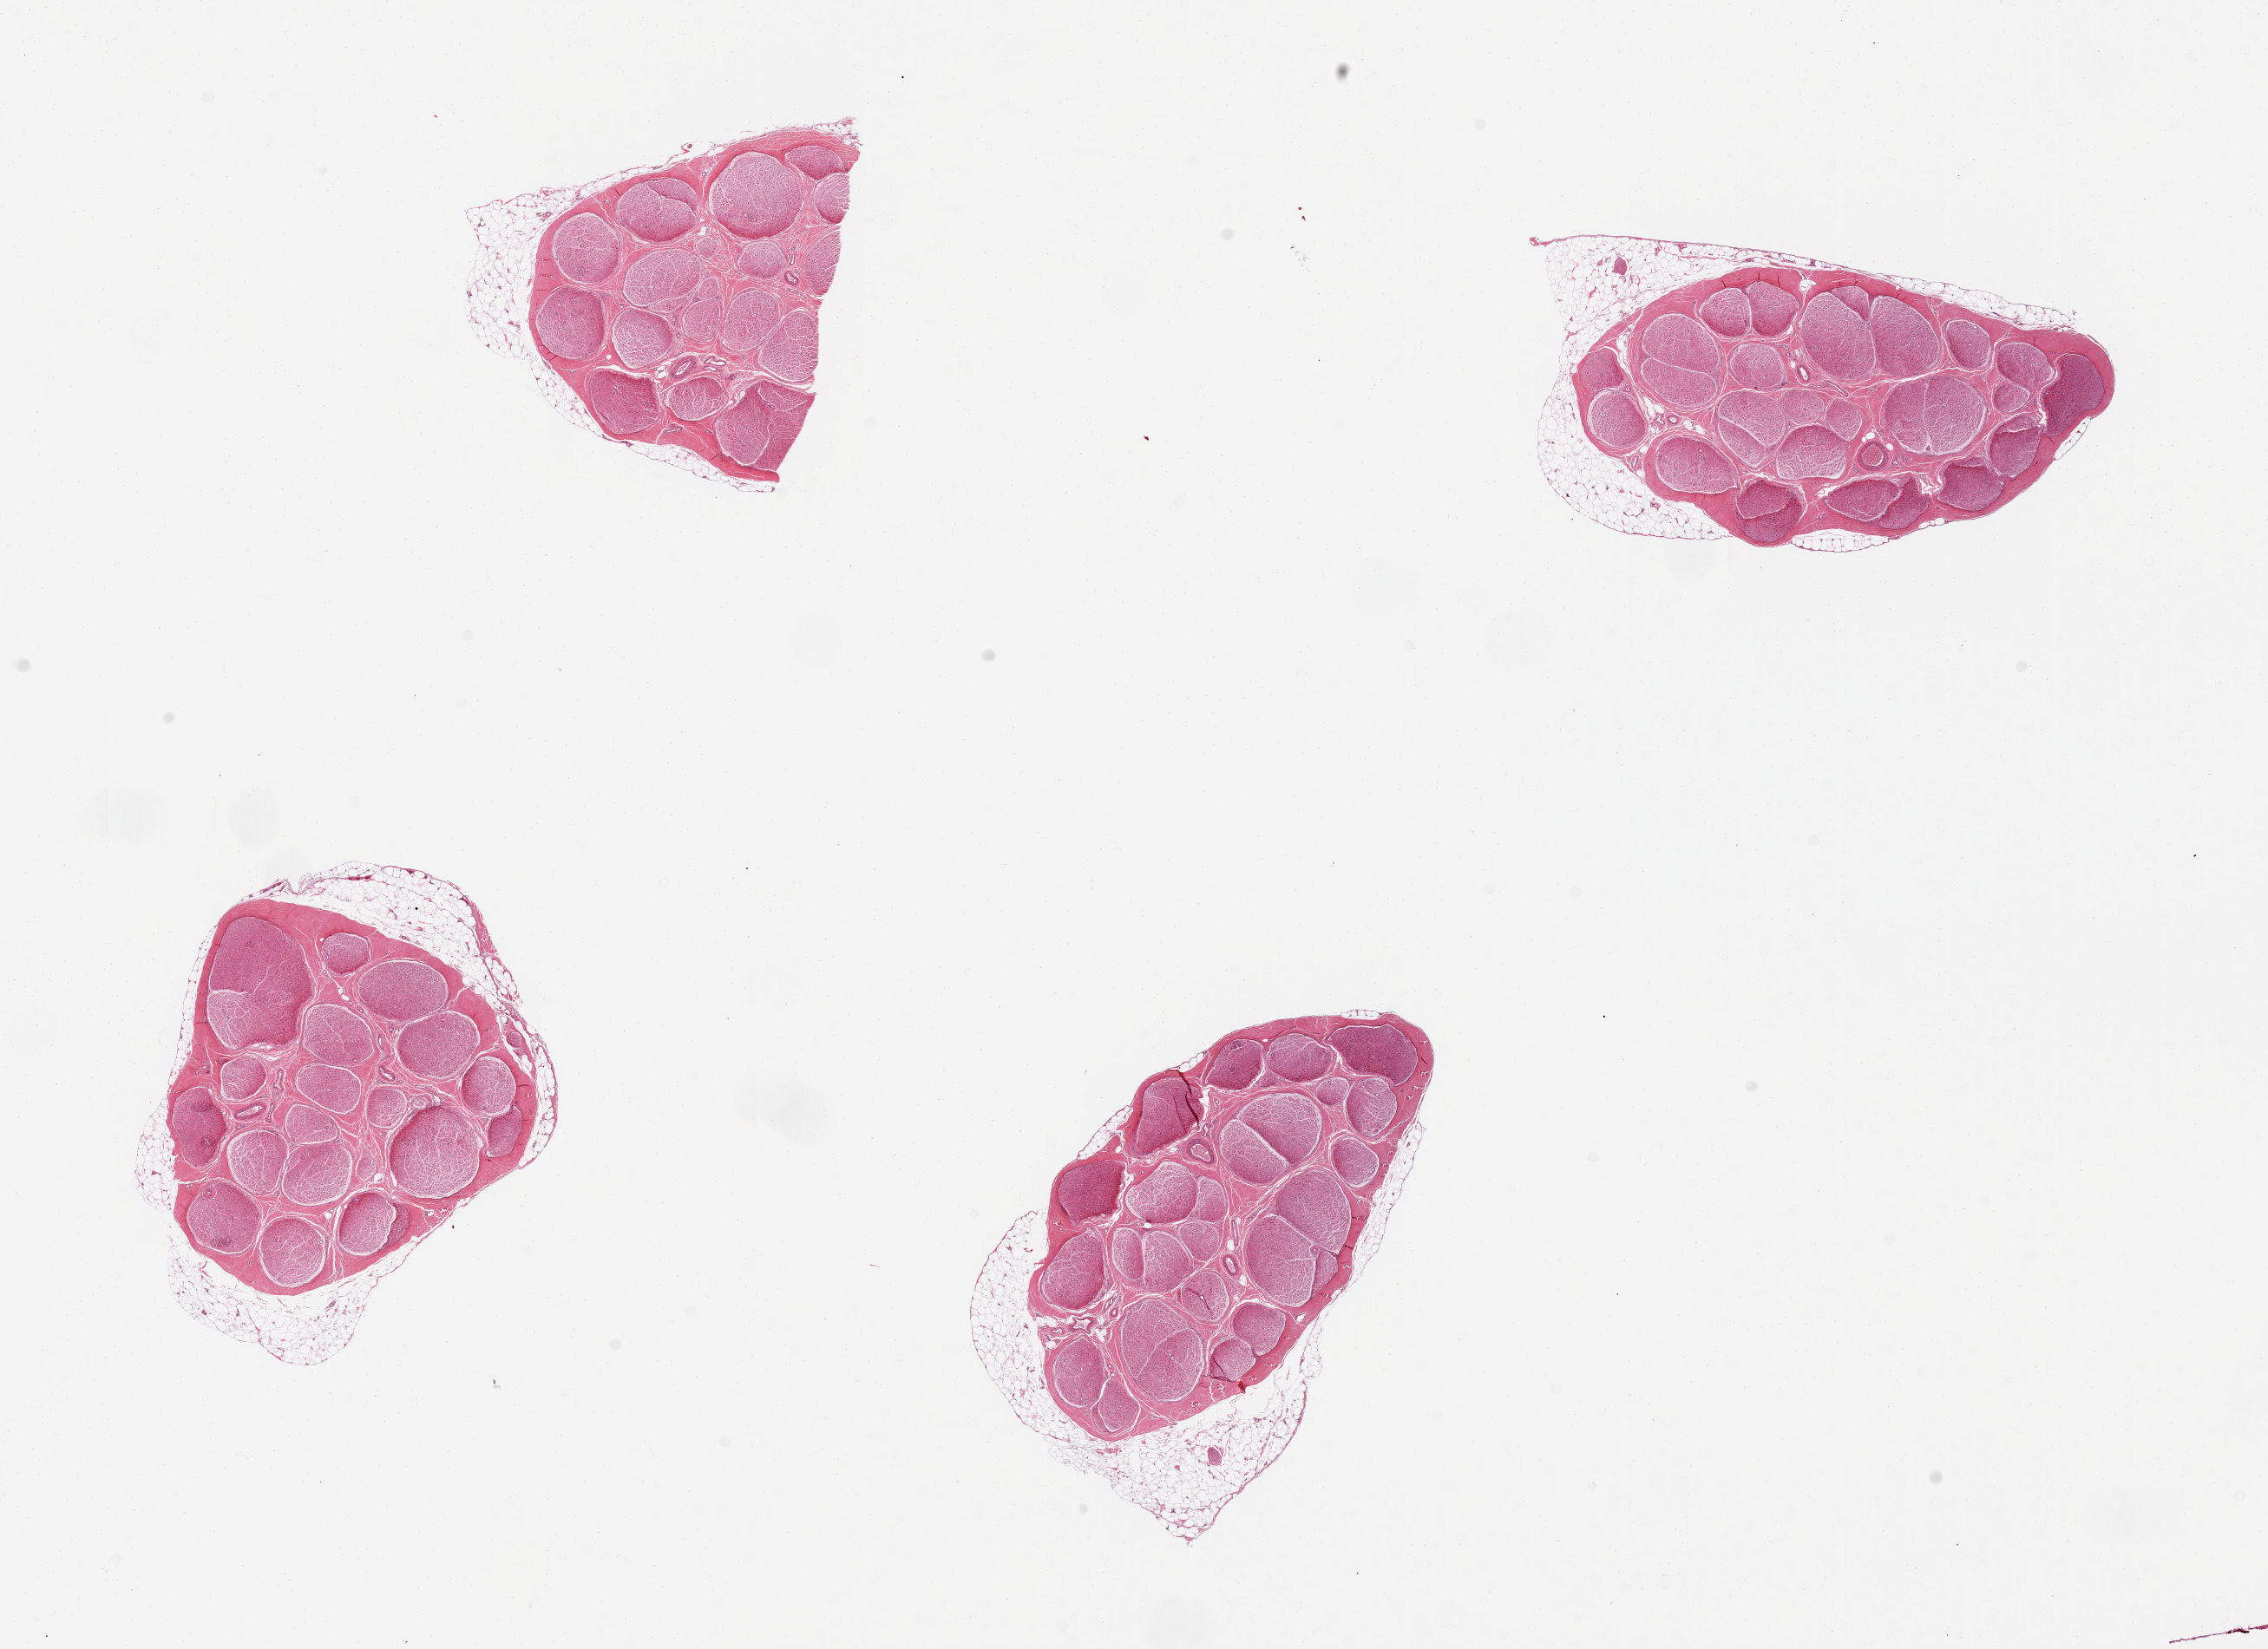
H&E whole-slide image — low-resolution overview of the scanned area, about 20.7 x 15.0 mm, PAXgene-fixed, paraffin-embedded tissue, section of tibial nerve (target tissue), tissue donor sample. Donor: male.
- review note (as recorded): 4 pieces, adherent nubbins of fat up to ~1mm